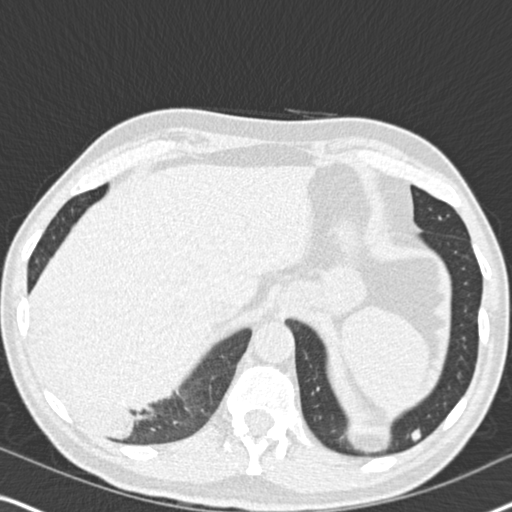
Low-dose screening chest CT, one axial slice; position 46 of 182 along the scan axis; reconstruction kernel B30f; 120 kVp; lung window (W 1500 / L -600 HU); 512 × 512 image matrix, field of view 330 × 330 mm.
Structures marked on this image (outlined manually by an expert reader):
- lesion 1 (tumor, lower lobe of right lung): box from (x=82, y=407) to (x=137, y=436) px